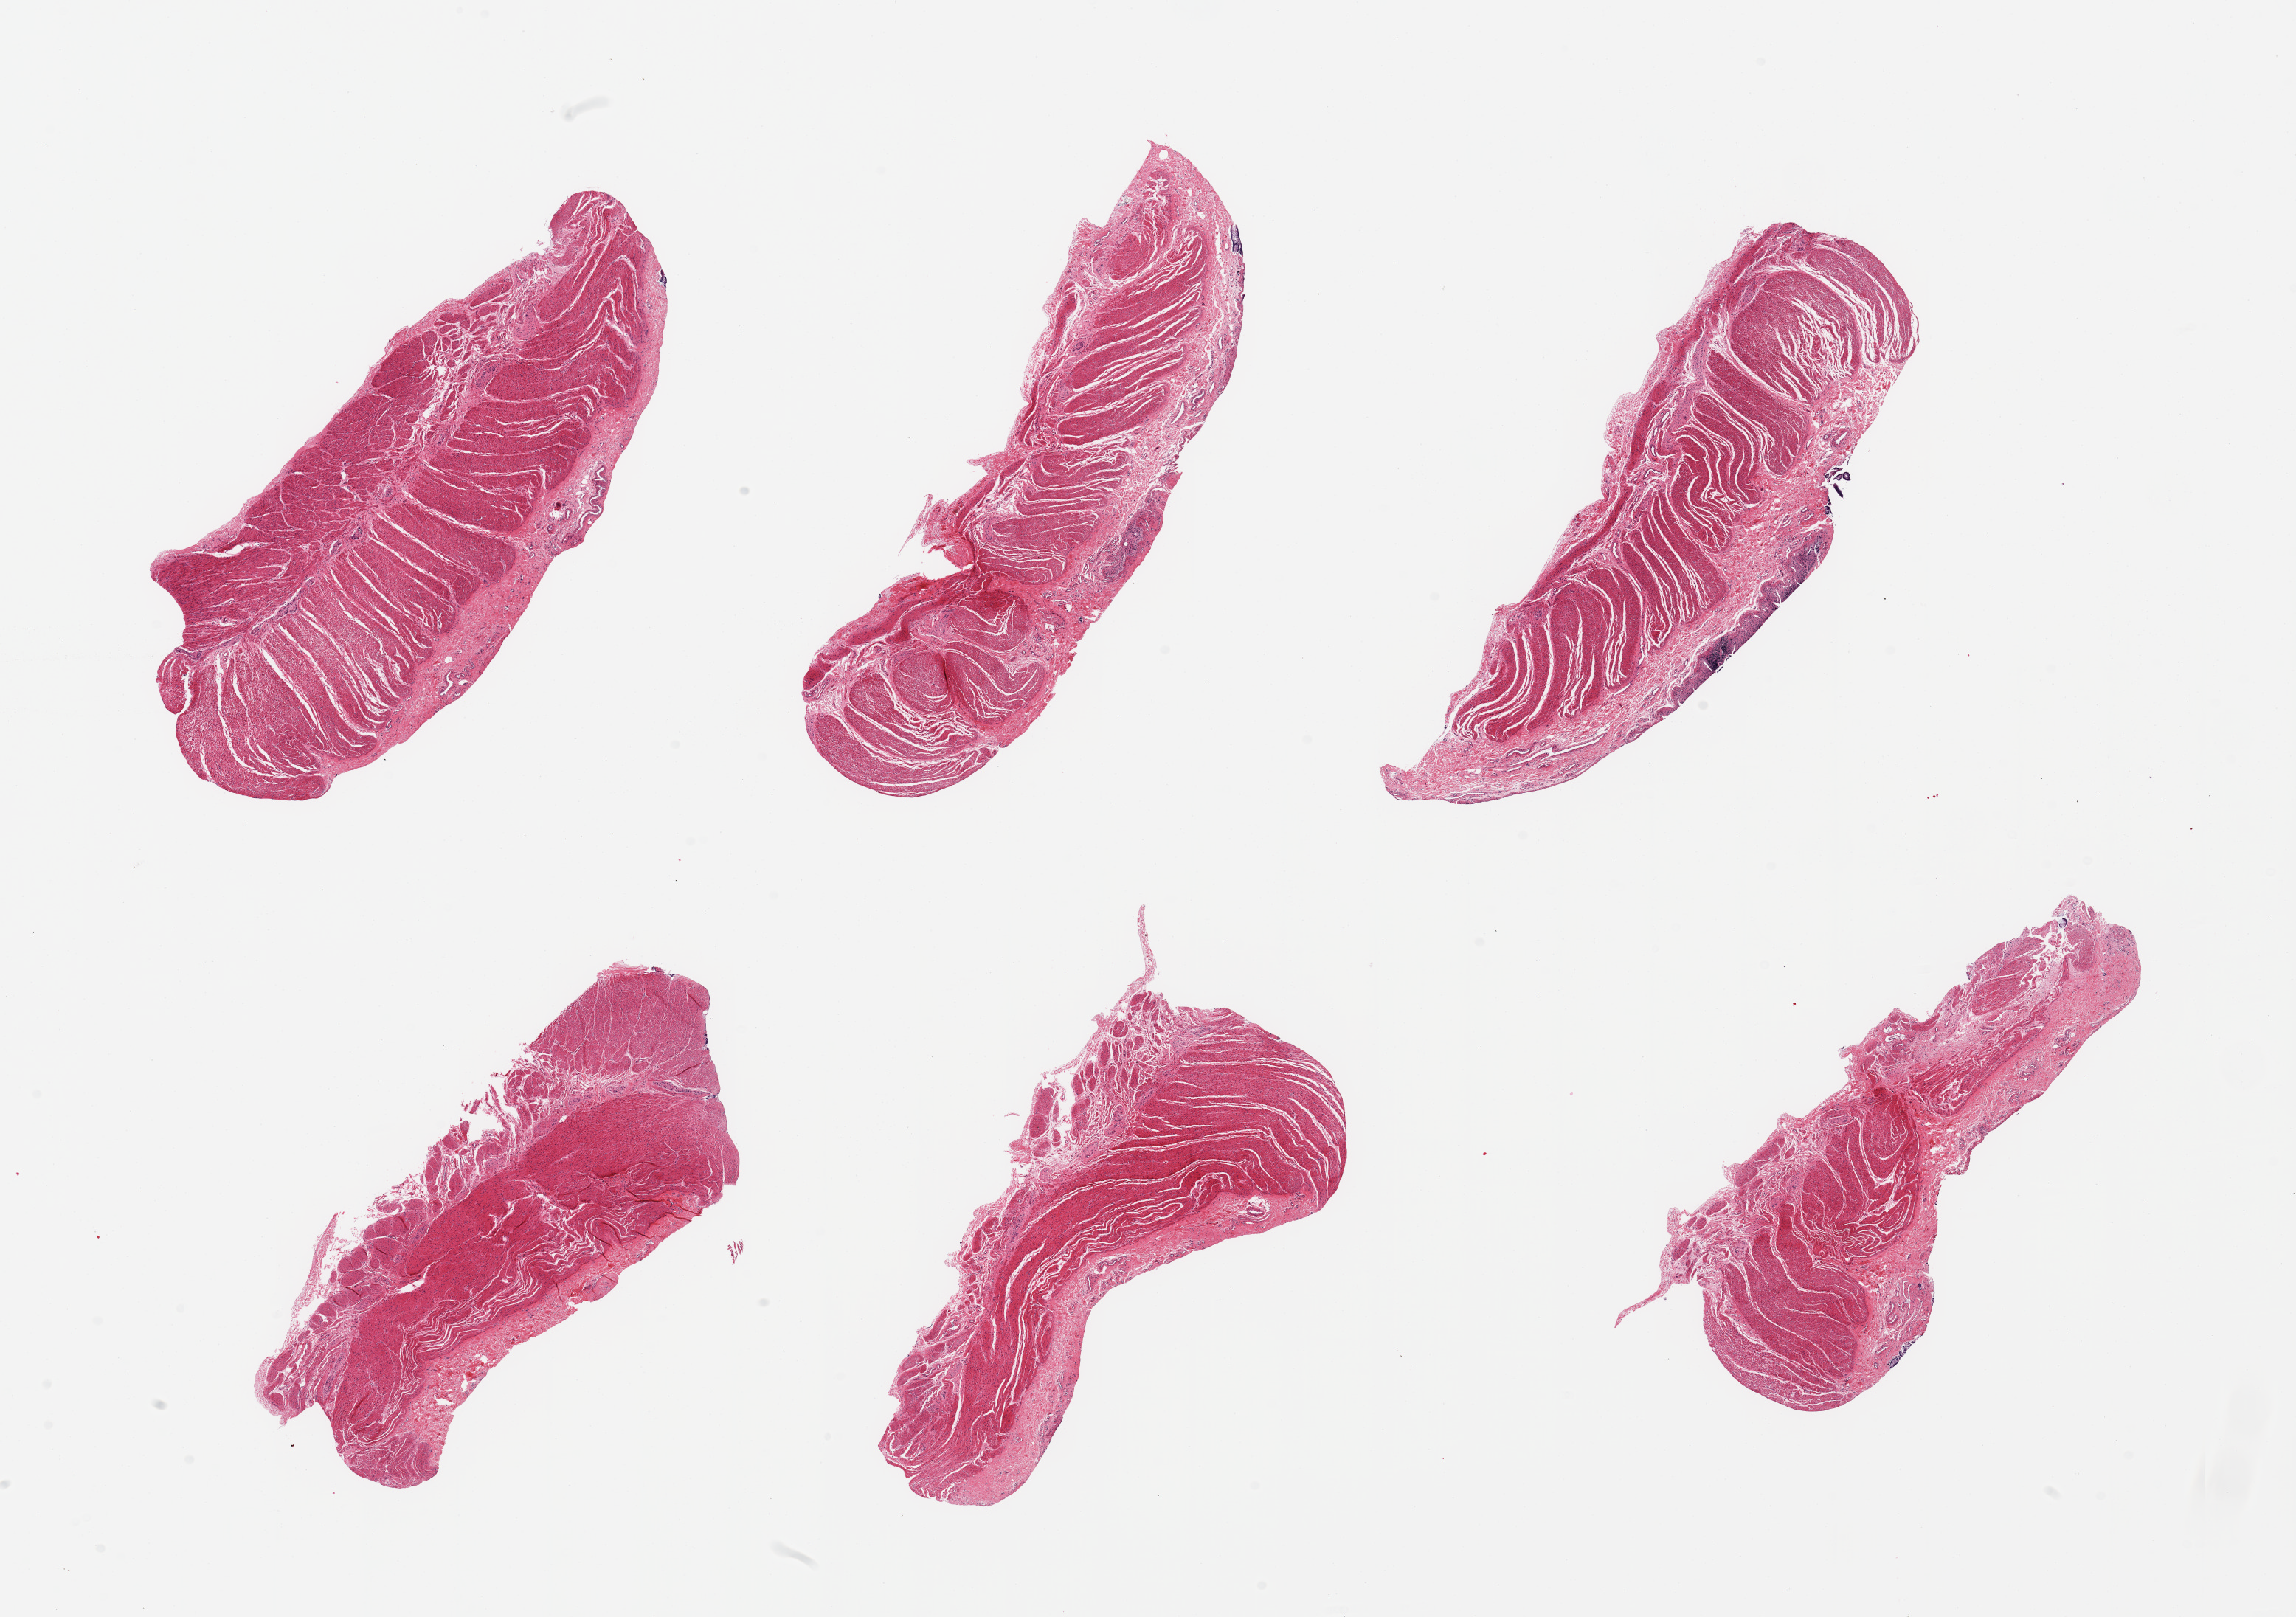
Whole-slide image, H&E stain, whole scanned area (about 24.6 x 17.3 mm) shown as a low-resolution overview, PAXgene-fixed paraffin-embedded (PFPE) section, target tissue: sigmoid colon, tissue donor sample.
Reviewer comment on this tissue sample: 6 pieces, confirmed target muscularis.